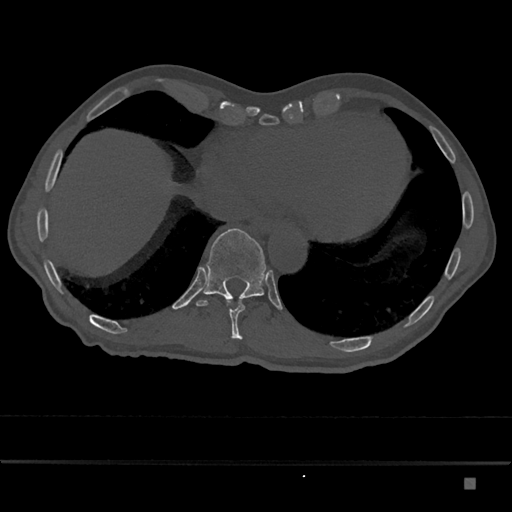
CT including the spine, one axial slice; slice 707 of 797 in the series (ordered by position); reconstruction kernel Br40s/3; bone window (W 1800 / L 400 HU); 512 × 512 image matrix, field of view 390 × 390 mm. Male patient, age 72 years. Case-level facts recorded for this patient, not image findings: primary cancer: prostate.
Outlined on this slice (semi-automatic segmentation, software-assisted and operator-edited):
- T10 vertebra: bounding box <226,298,245,340> (left, top, right, bottom; pixels)
- T11 vertebra: <196,228,267,306>